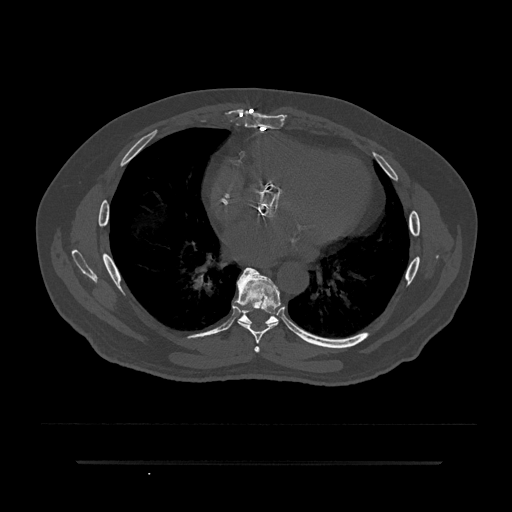
CT including the spine, one axial slice; slice 459 of 797 in the series (ordered by position); reconstruction kernel Br40s/3; 120 kVp; bone window (W 1800 / L 400 HU); 0.5 mm slice thickness; 512 × 512 image matrix, field of view 464 × 464 mm. Patient: male, 59 years. From the clinical record (not read from this slice): primary cancer: bile ducts.
Outlined on this slice (semi-automatic segmentation, software-assisted and operator-edited):
- T6 vertebra: bounding box (x1, y1, x2, y2) in pixels: (254, 346, 260, 353)
- T7 vertebra: (233, 267, 281, 344)
- T8 vertebra: (223, 308, 297, 334)